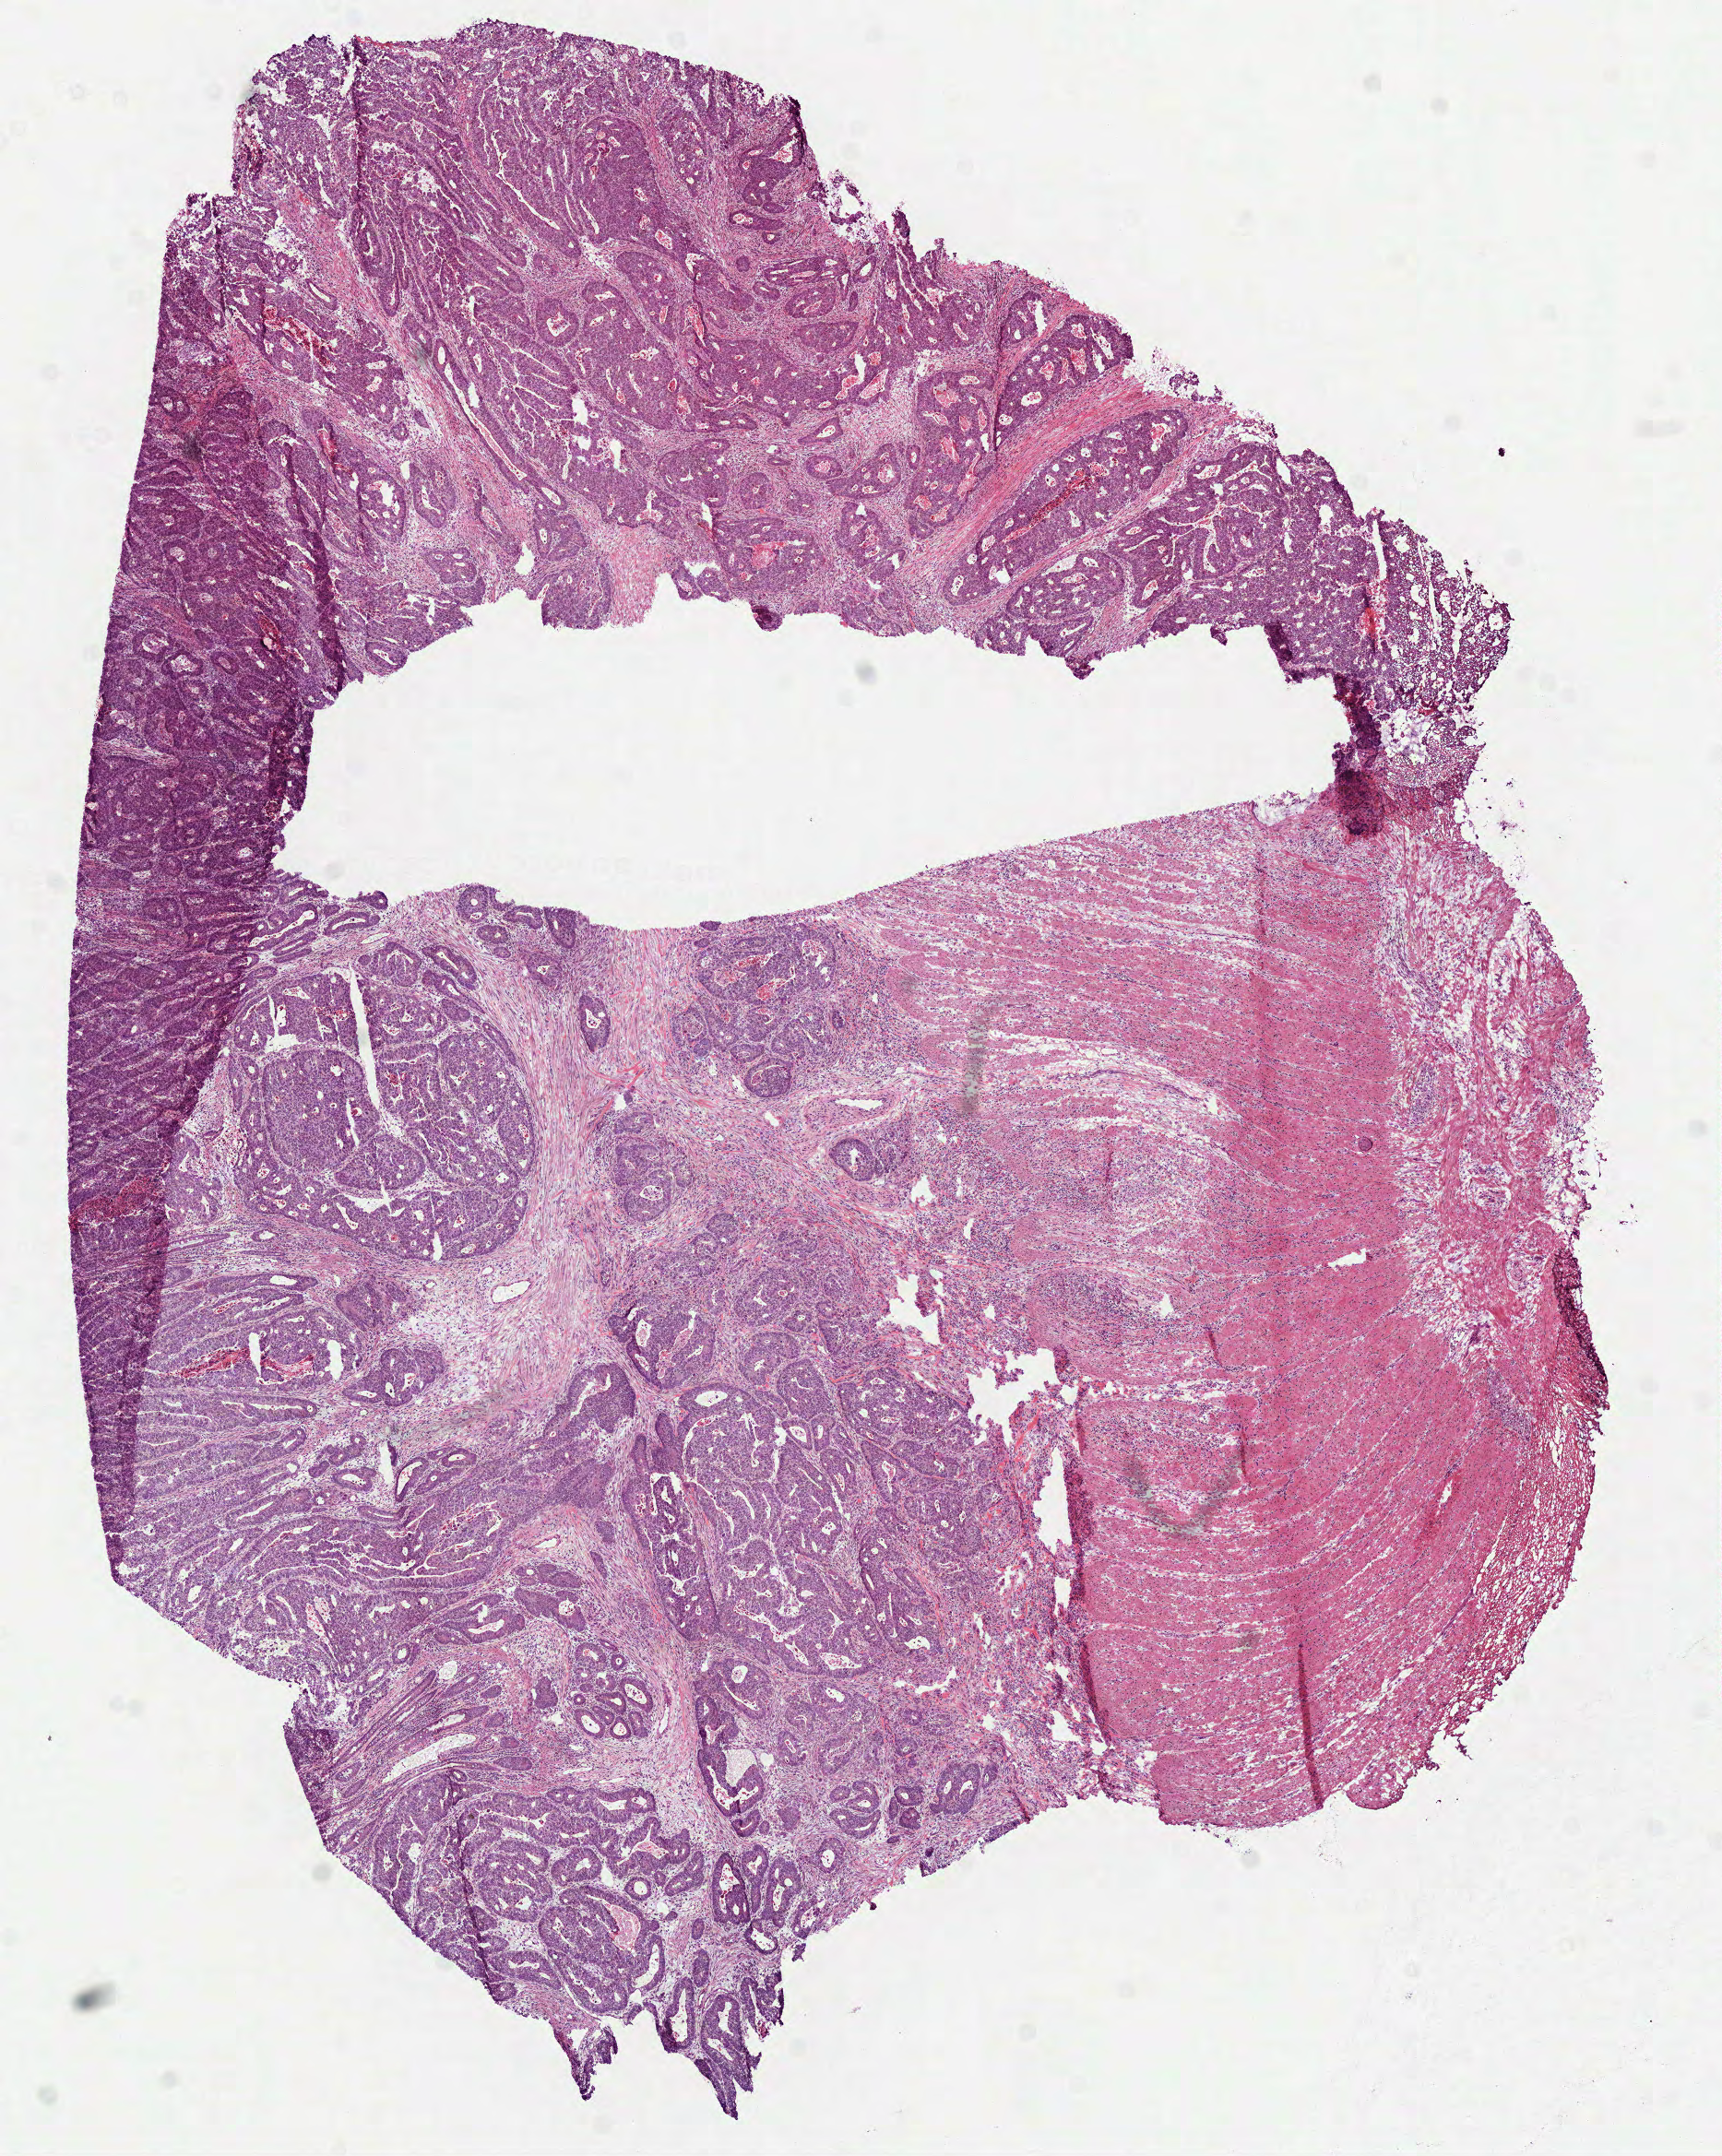
Whole-slide histology image, Hematoxylin and eosin (H&E) stained, shown as a low-resolution overview of the whole scanned area (about 7.5 x 9.4 mm, slide scanned at 40x). Frozen section from the bottom of the tissue portion. Primary tumour sample from the colon. Male, age 56 years at initial diagnosis. Composition of this section per pathologist review: tumour cells 65%, tumour nuclei 65%, normal cells 30%, stromal cells 0%, necrosis 5%. Infiltration values recorded for this section: lymphocyte infiltration 10%, monocyte infiltration 2%, neutrophil infiltration 10%.
Lymph nodes positive (case pathology): 0 of 21 examined. Diagnosis: Adenocarcinoma, NOS (descending colon). TNM: T3 N0 M1a. AJCC pathologic stage: IVA (7th edition).